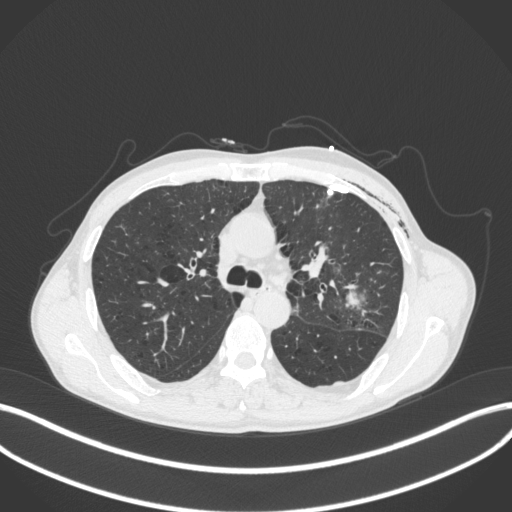
Chest CT, one axial slice. Position 265 of 416 along the scan axis. Lung window (W 1500 / L -600 HU). 1 mm slice thickness. 512 × 512 image matrix, field of view 400 × 400 mm. Male patient, age 58 years. From the clinical record (not read from this slice): clinical TNM (as recorded): T3 N0 M0.
Structures marked on this image (rectangle marked by the reading radiologist):
- lung tumour (recorded histology: adenocarcinoma): bounding box (x1, y1, x2, y2) in pixels: (338, 278, 369, 313)